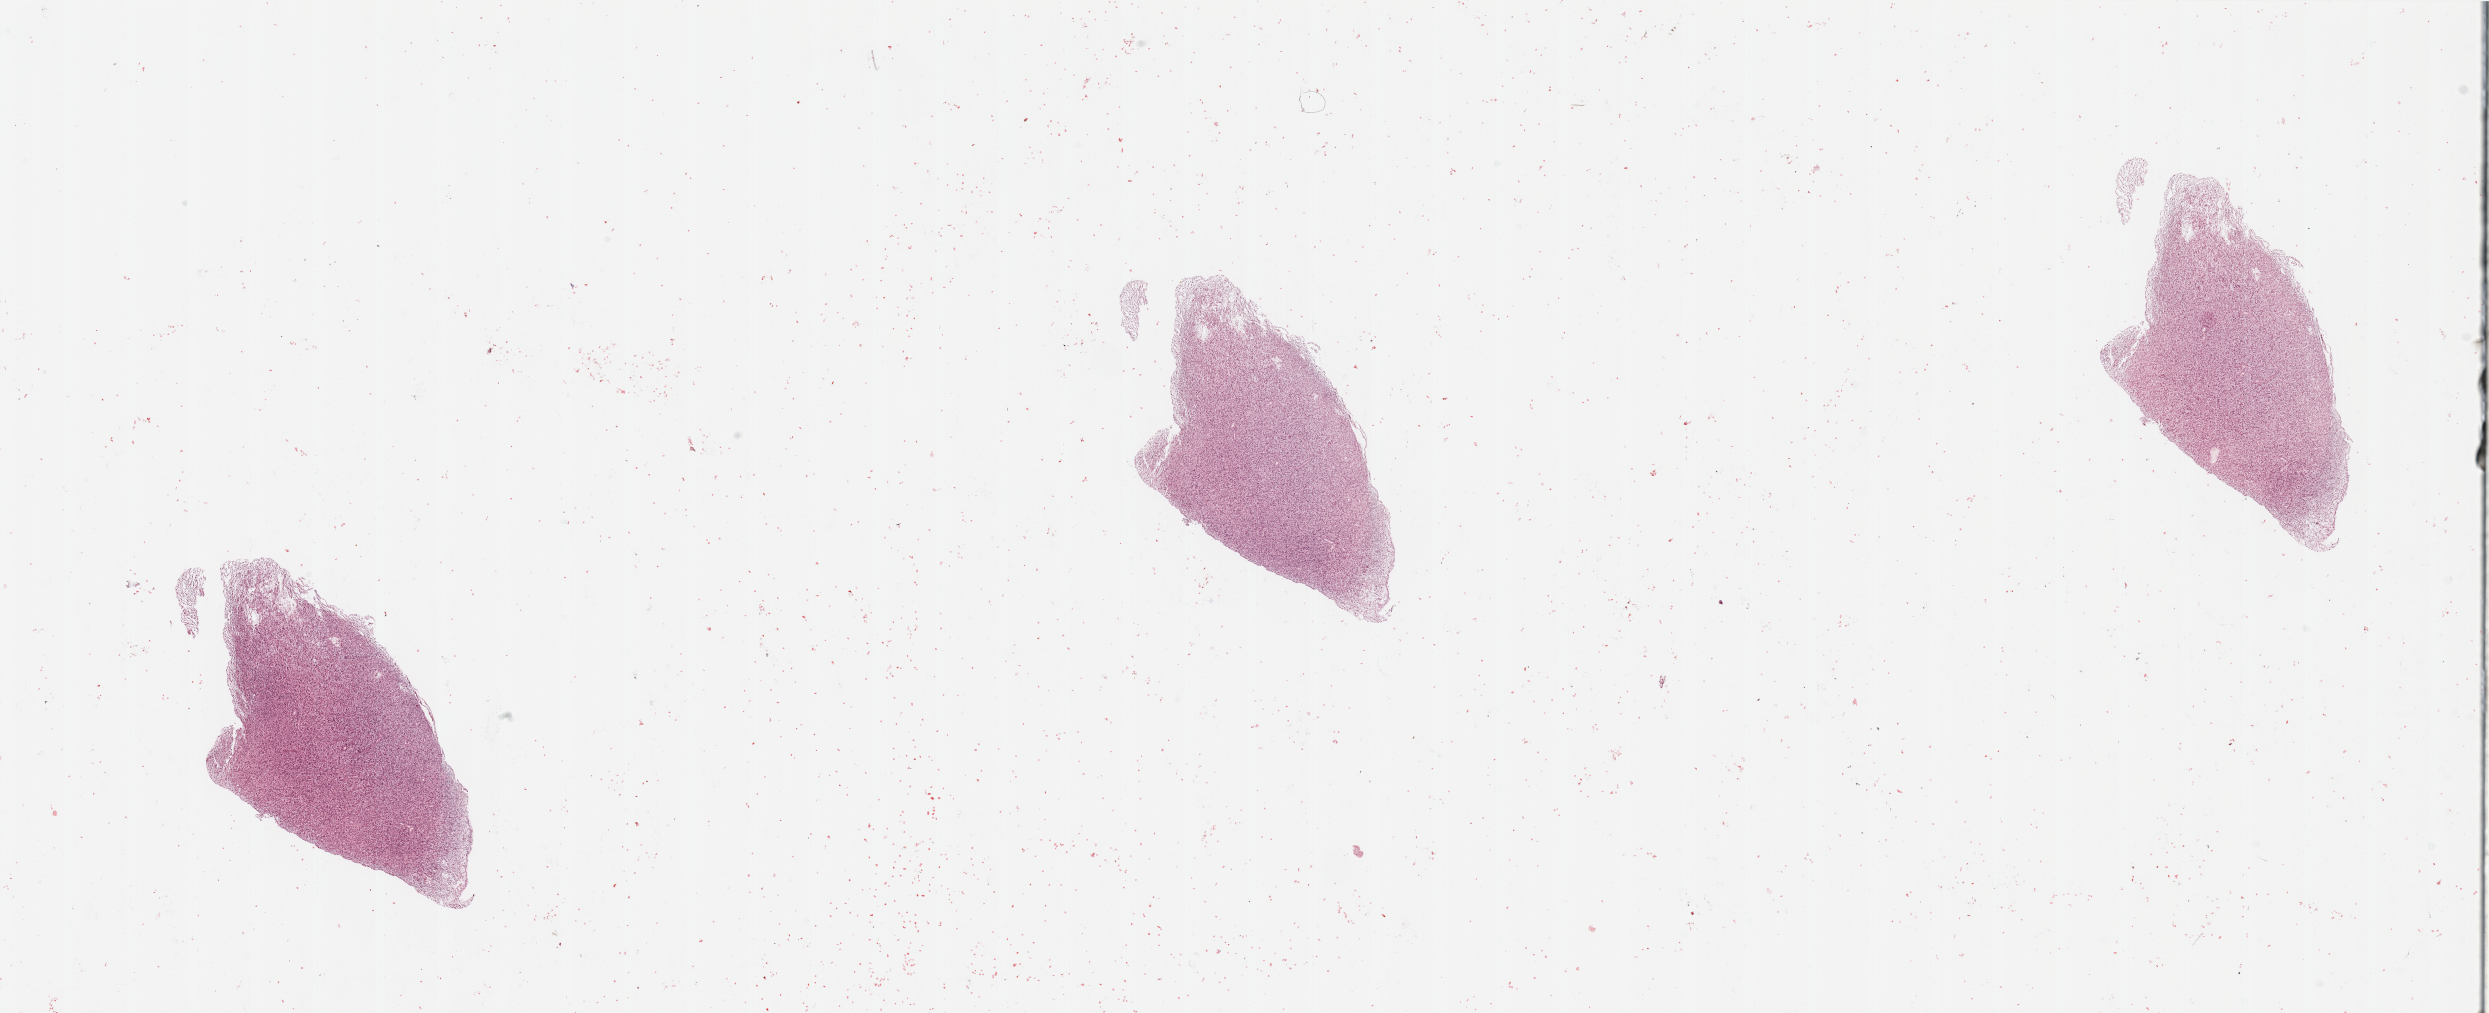
Hematoxylin and eosin (H&E) stained whole-slide image, a low-resolution overview of the entire scanned area, about 39.4 x 16.0 mm. Tumour tissue sample, sampled site: brain. 65-year-old male patient. Composition of this section per pathologist review: tumour nuclei 85%, necrosis 0%.
- primary tumour site (as recorded): temporal lobe
- histologic diagnosis: Glioblastoma